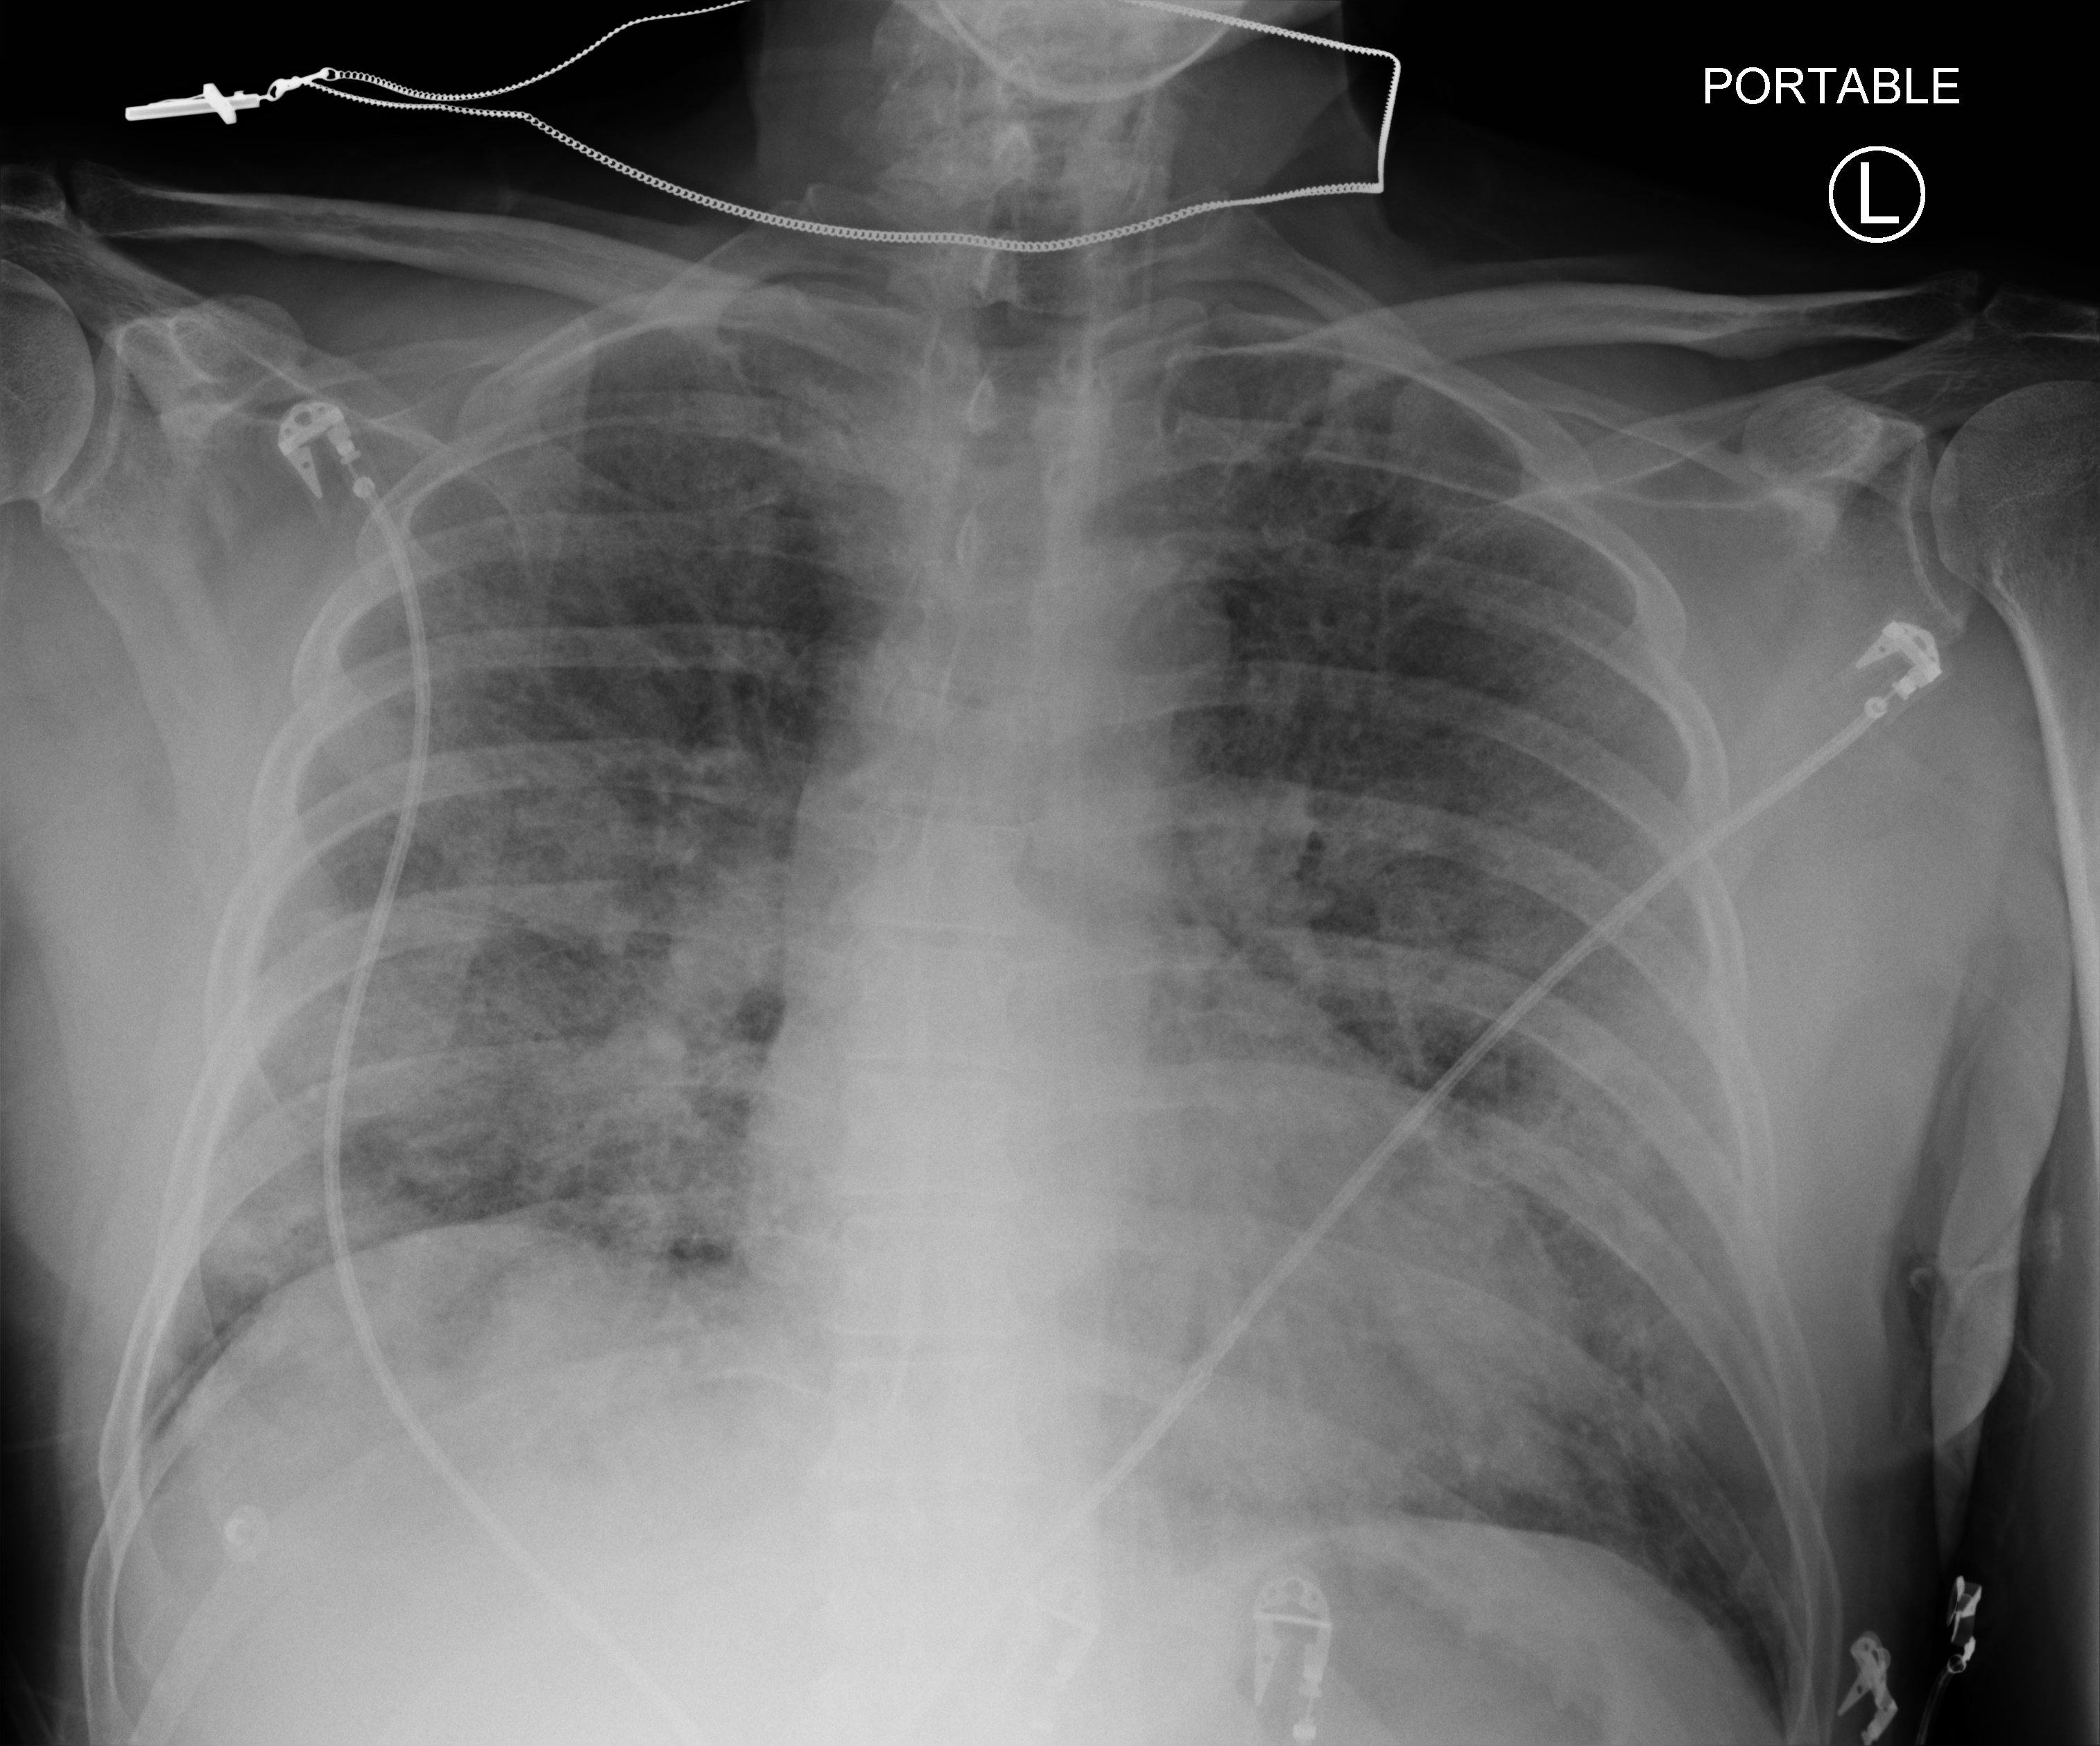
Bedside chest radiograph (computed radiography); anteroposterior (AP) projection. Male patient hospitalised with COVID-19, age 60–74 years.
Admission-level facts for this patient (not findings on this image; timing relative to this image not recorded):
- admitted to intensive care during this hospital stay: no
- mechanically ventilated during this hospital stay: no
- hypertension (admission record): no